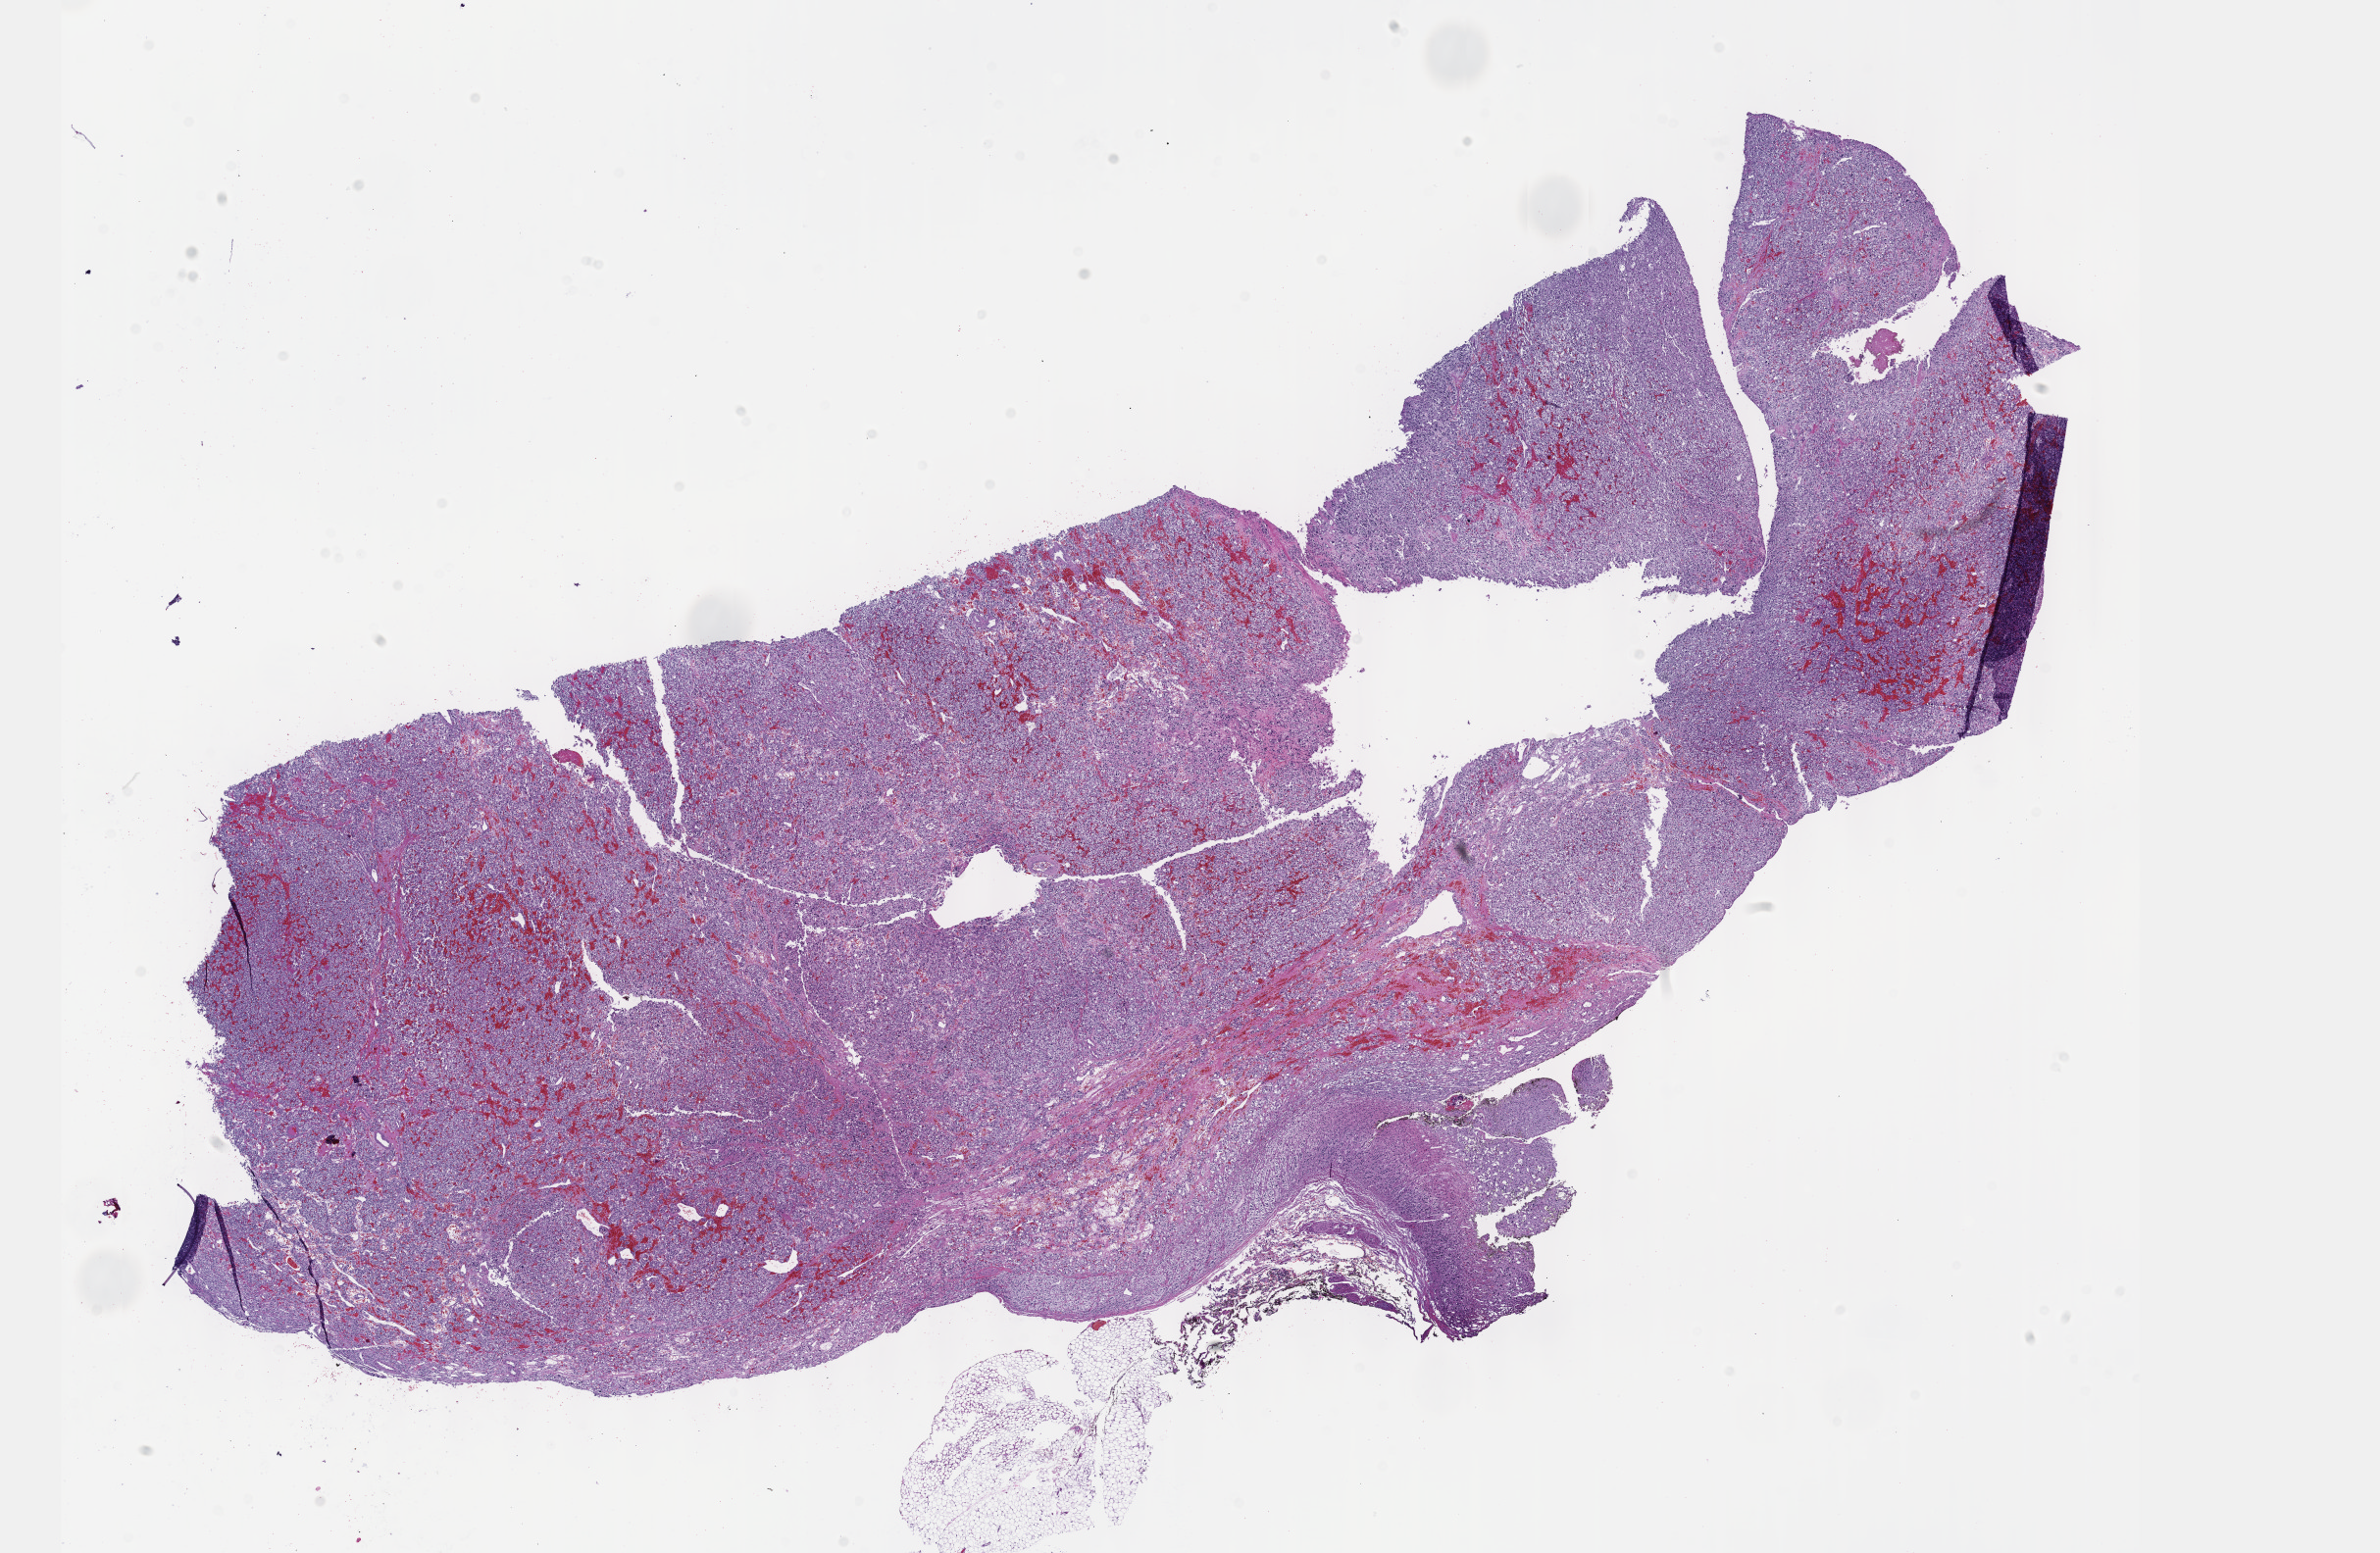
Digitized Hematoxylin and eosin (H&E) stained tissue section (whole slide), whole scanned area (about 19.6 x 12.8 mm, acquisition: 40x scan) shown as a low-resolution overview. FFPE section. Primary tumour sample from the adrenal gland. Patient: female, age at initial diagnosis 30 years.
• histologic diagnosis: Pheochromocytoma, NOS
• laterality: right